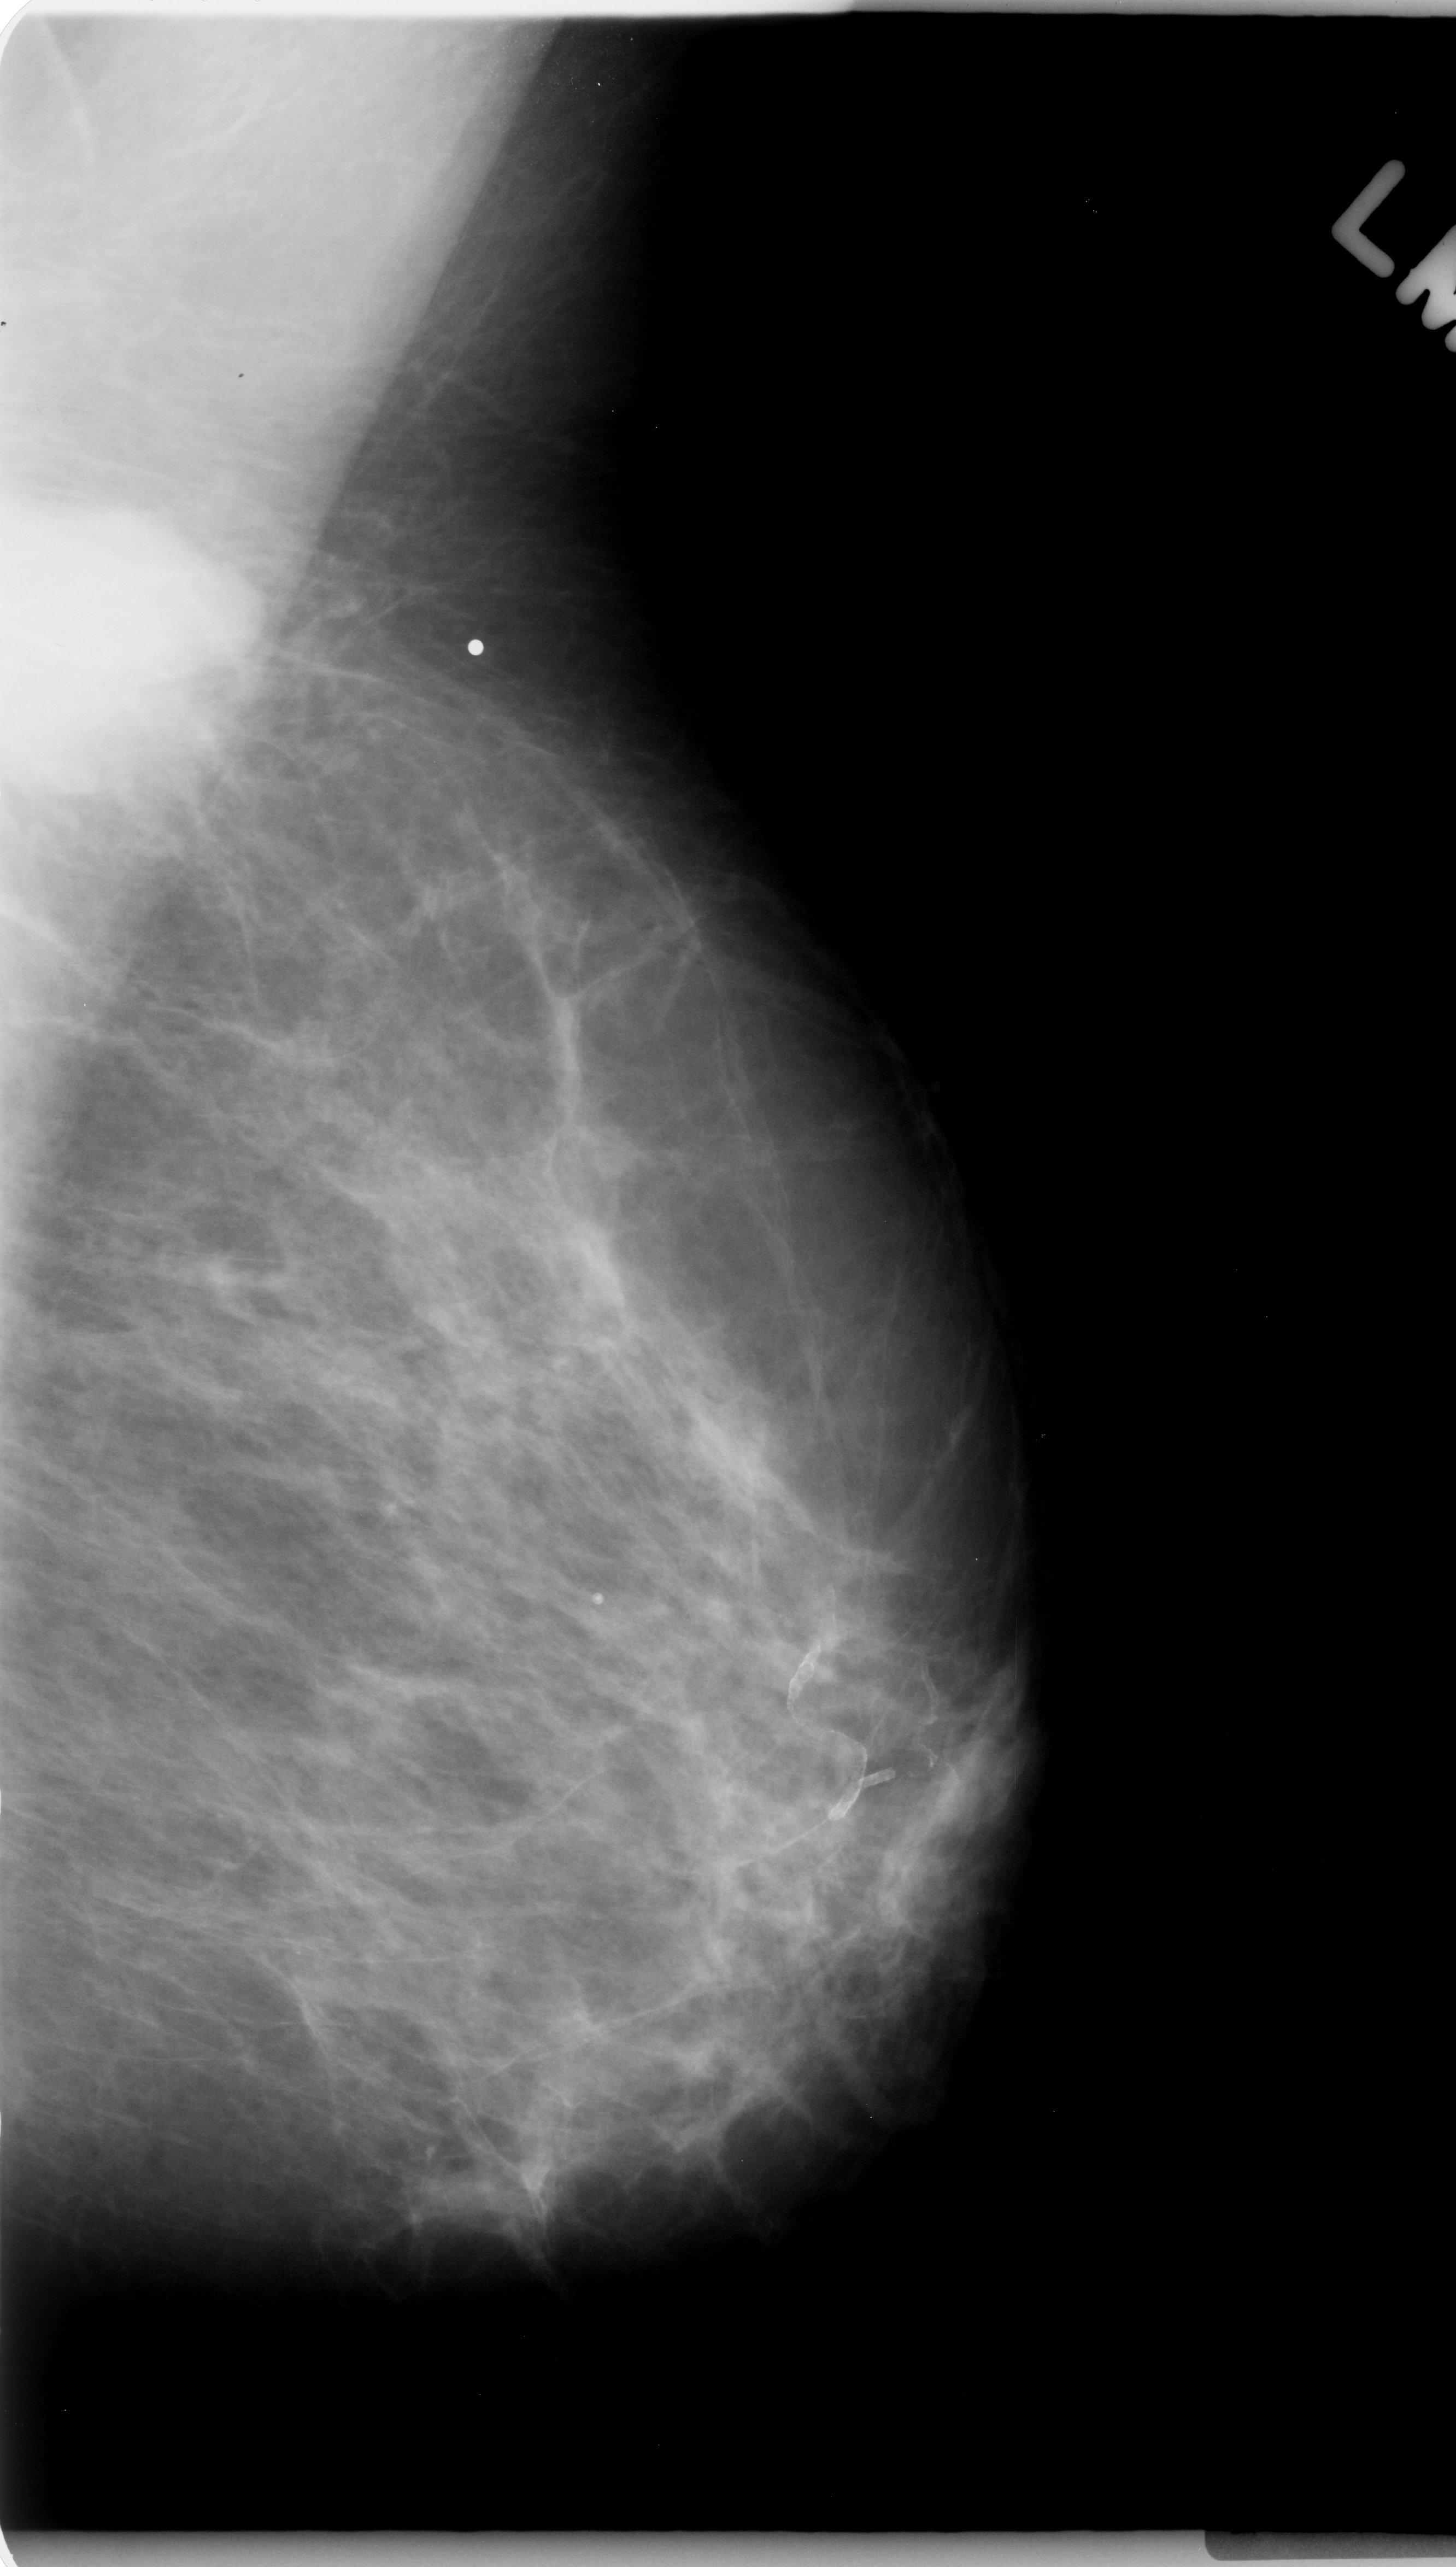
Scanned film-screen mammogram, left breast, mediolateral oblique (MLO) view, breast composition: scattered fibroglandular densities (BI-RADS density category 2 of 4).
Abnormality record for this image: mass, shape lobulated, margins microlobulated; BI-RADS assessment category 5; subtlety rating 5 on a 1 (subtle) to 5 (obvious) scale; pathology result (as recorded, not read from the image): malignant.